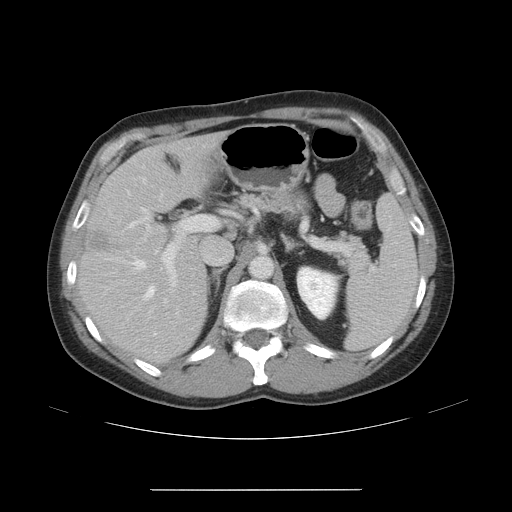
Contrast-enhanced abdominal CT, one axial slice. Slice 29 of 48 in the series (ordered by position). Reconstruction kernel STANDARD. Intravenous contrast given. Soft-tissue window (W 400 / L 40 HU). 5 mm slice thickness. 512 × 512 image matrix, field of view 409 × 409 mm. Male patient, age 56 years. From the clinical record (not read from this slice): diagnosis: colorectal cancer liver metastases, imaged before liver resection; multiple liver metastases: yes; largest metastasis: 1.8 cm; chemotherapy before resection: yes.
Structures marked on this image (outlined manually by an expert reader):
- hepatic veins: box from (x=105, y=176) to (x=164, y=336) px
- liver: (x=80, y=136)–(x=218, y=361)
- planned liver remnant (the part of the liver to remain after resection): (x=81, y=135)–(x=218, y=361)
- portal vein (with intrahepatic branches): (x=126, y=189)–(x=221, y=303)
- liver metastasis: (x=91, y=233)–(x=112, y=252)